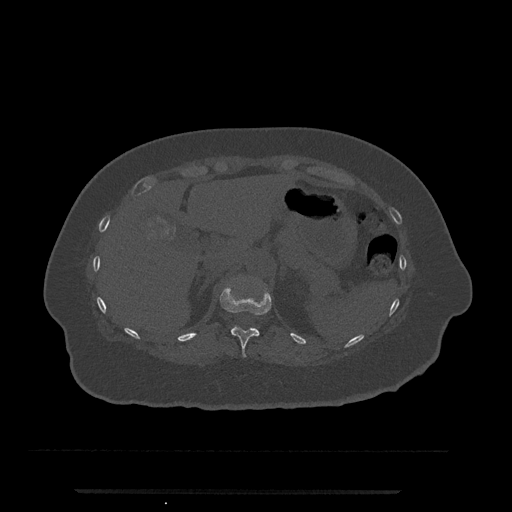
CT including the spine, one axial slice; slice 215 of 797 in the series (ordered by position); reconstruction kernel Br40s/3; 120 kVp; bone window (W 1800 / L 400 HU); 512 × 512 image matrix, field of view 440 × 440 mm. Female patient, age 51 years. From the clinical record (not read from this slice): primary cancer: neuro.
Structures marked on this image (semi-automatic segmentation, software-assisted and operator-edited):
- T11 vertebra: bounding box [x1, y1, x2, y2] px = [220, 287, 272, 358]